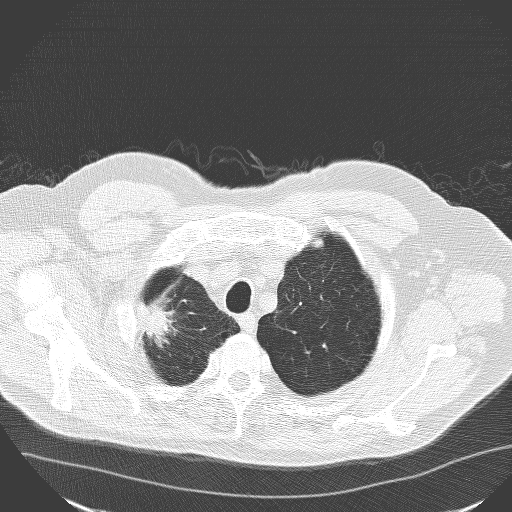
Low-dose screening chest CT, axial slice; first (baseline) screen; lung window (W 1500 / L -600 HU); 3.2 mm slice thickness; lung (sharp) reconstruction kernel (D); slice 142 of 160 in the series. Male, age 71 years at enrolment.
• Lesion marked by an expert reader, bounding box [x1, y1, x2, y2] px = [118, 288, 189, 361].
• Reader record for this screening exam (exam-level; its link to the box is not recorded): non-calcified nodule or mass ≥4 mm, right upper lobe, 30 × 25 mm, spiculated (stellate) margins, soft tissue attenuation.
• Official screen result: positive, change unspecified: nodule(s) >= 4 mm or enlarging nodule(s), mass(es), or other non-specific abnormalities suspicious for lung cancer.
• Lung cancer was diagnosed 182 days after this screen: squamous cell carcinoma, NOS, right upper lobe, poorly differentiated (G3), stage IA (AJCC 6th edition), 30 mm at pathology.